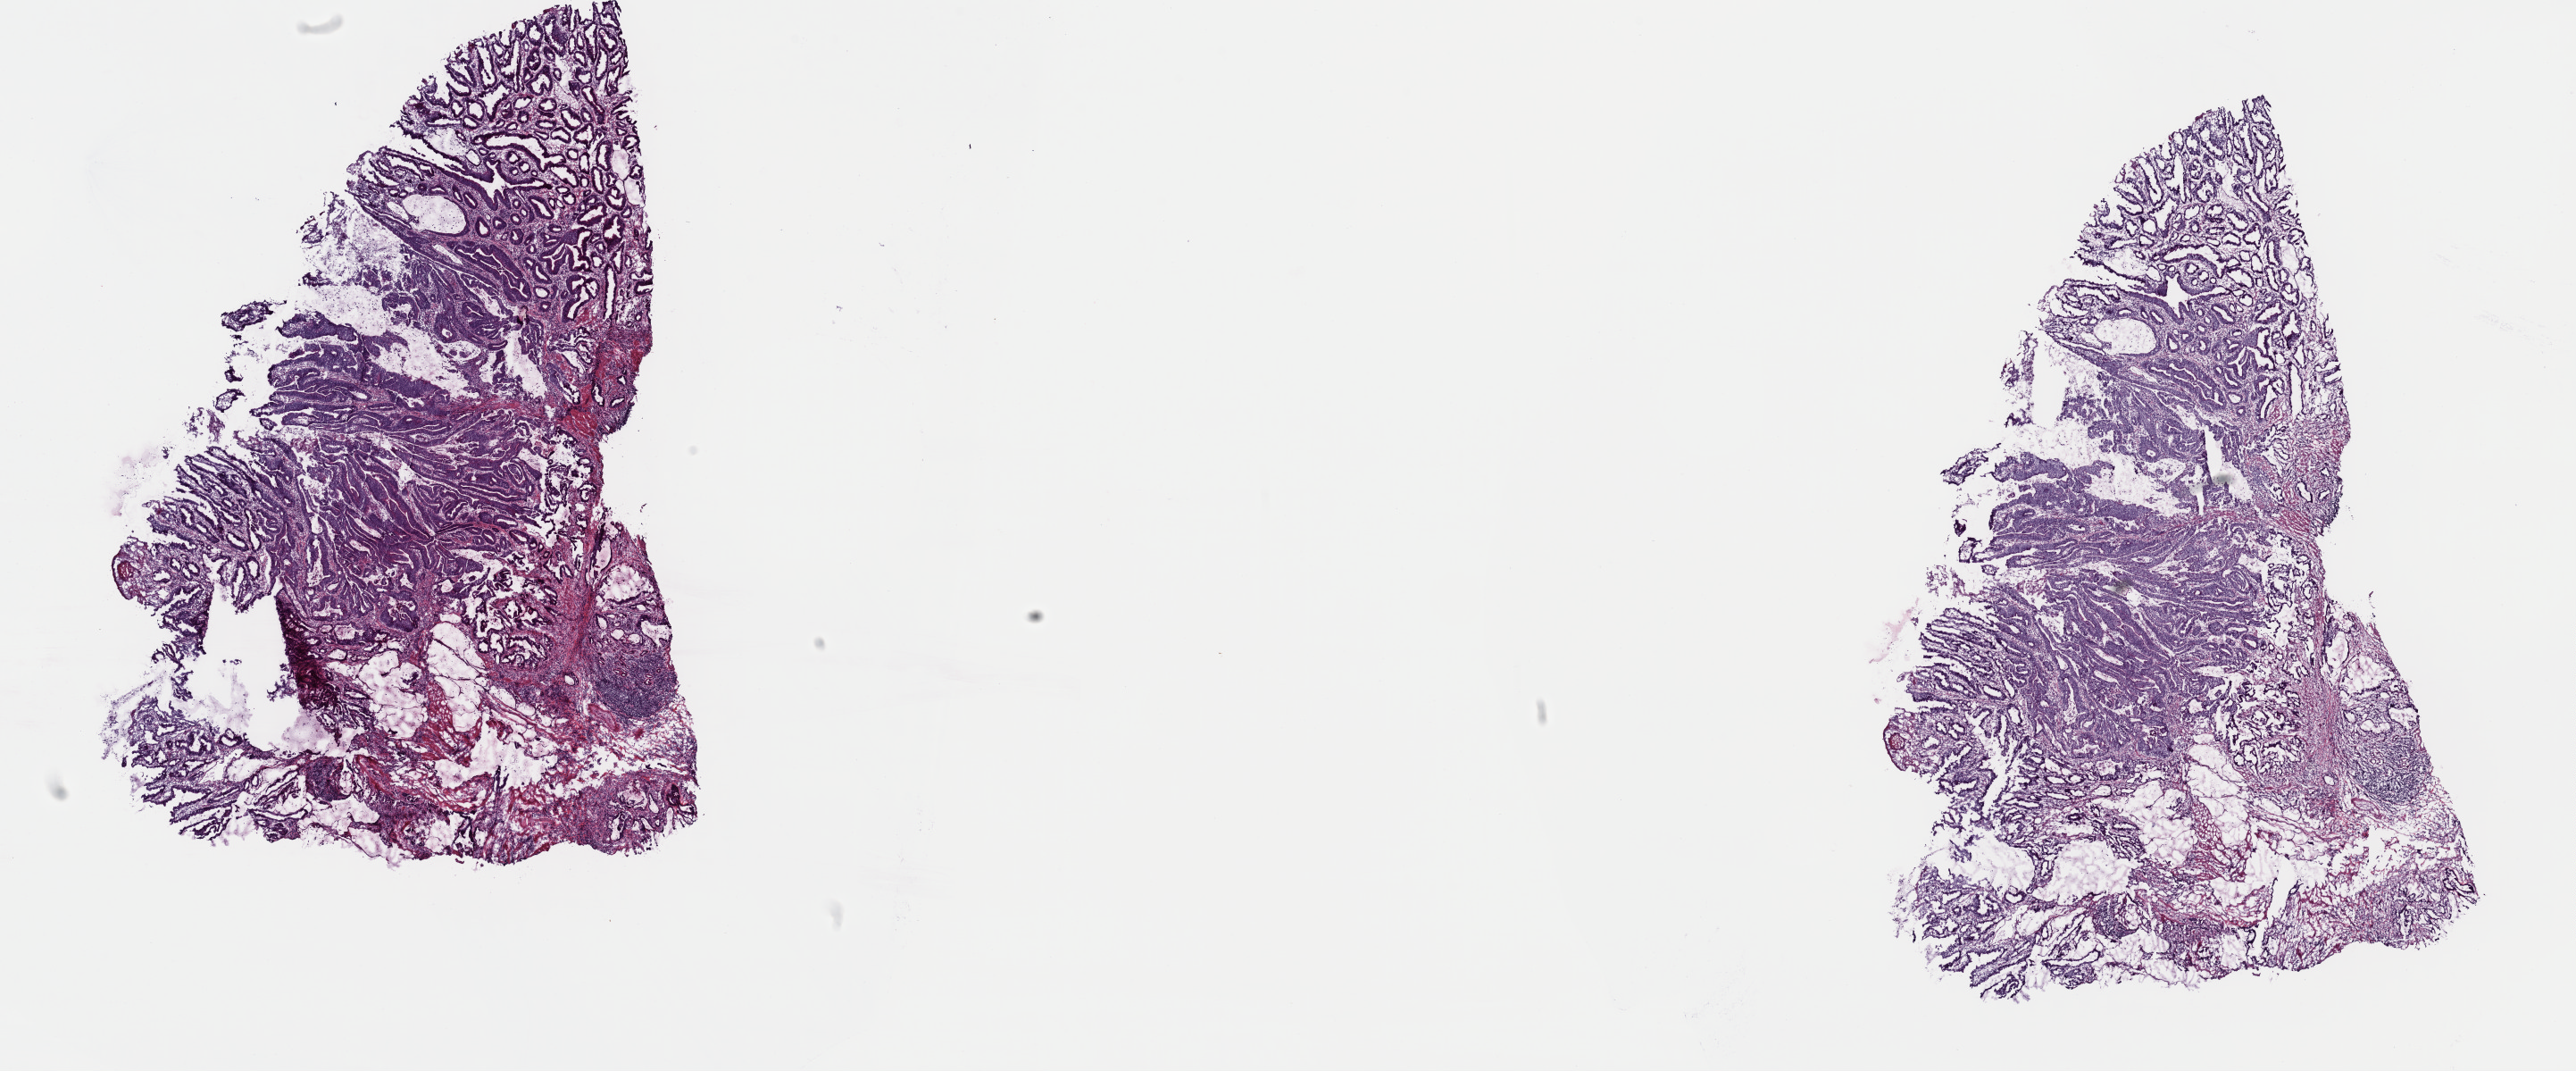
Whole-slide histology image, Hematoxylin and eosin (H&E) stained — low-resolution overview of the scanned area, about 22.8 x 9.5 mm. Frozen section. Primary tumour sample from the esophagus. Male patient; age at initial diagnosis 79 years. Histologic grade: G2 (moderately differentiated). Composition of this section per pathologist review: tumour cells 100%, tumour nuclei 75%, normal cells 0%, stromal cells 0%, necrosis 0%. Inflammatory infiltration, as recorded: lymphocyte infiltration 0%, monocyte infiltration 0%, neutrophil infiltration 0%.
Lymph nodes positive (case pathology): 8 of 20 examined. Histologic diagnosis: Adenocarcinoma, NOS (lower third of esophagus). AJCC pathologic stage: IIIC.